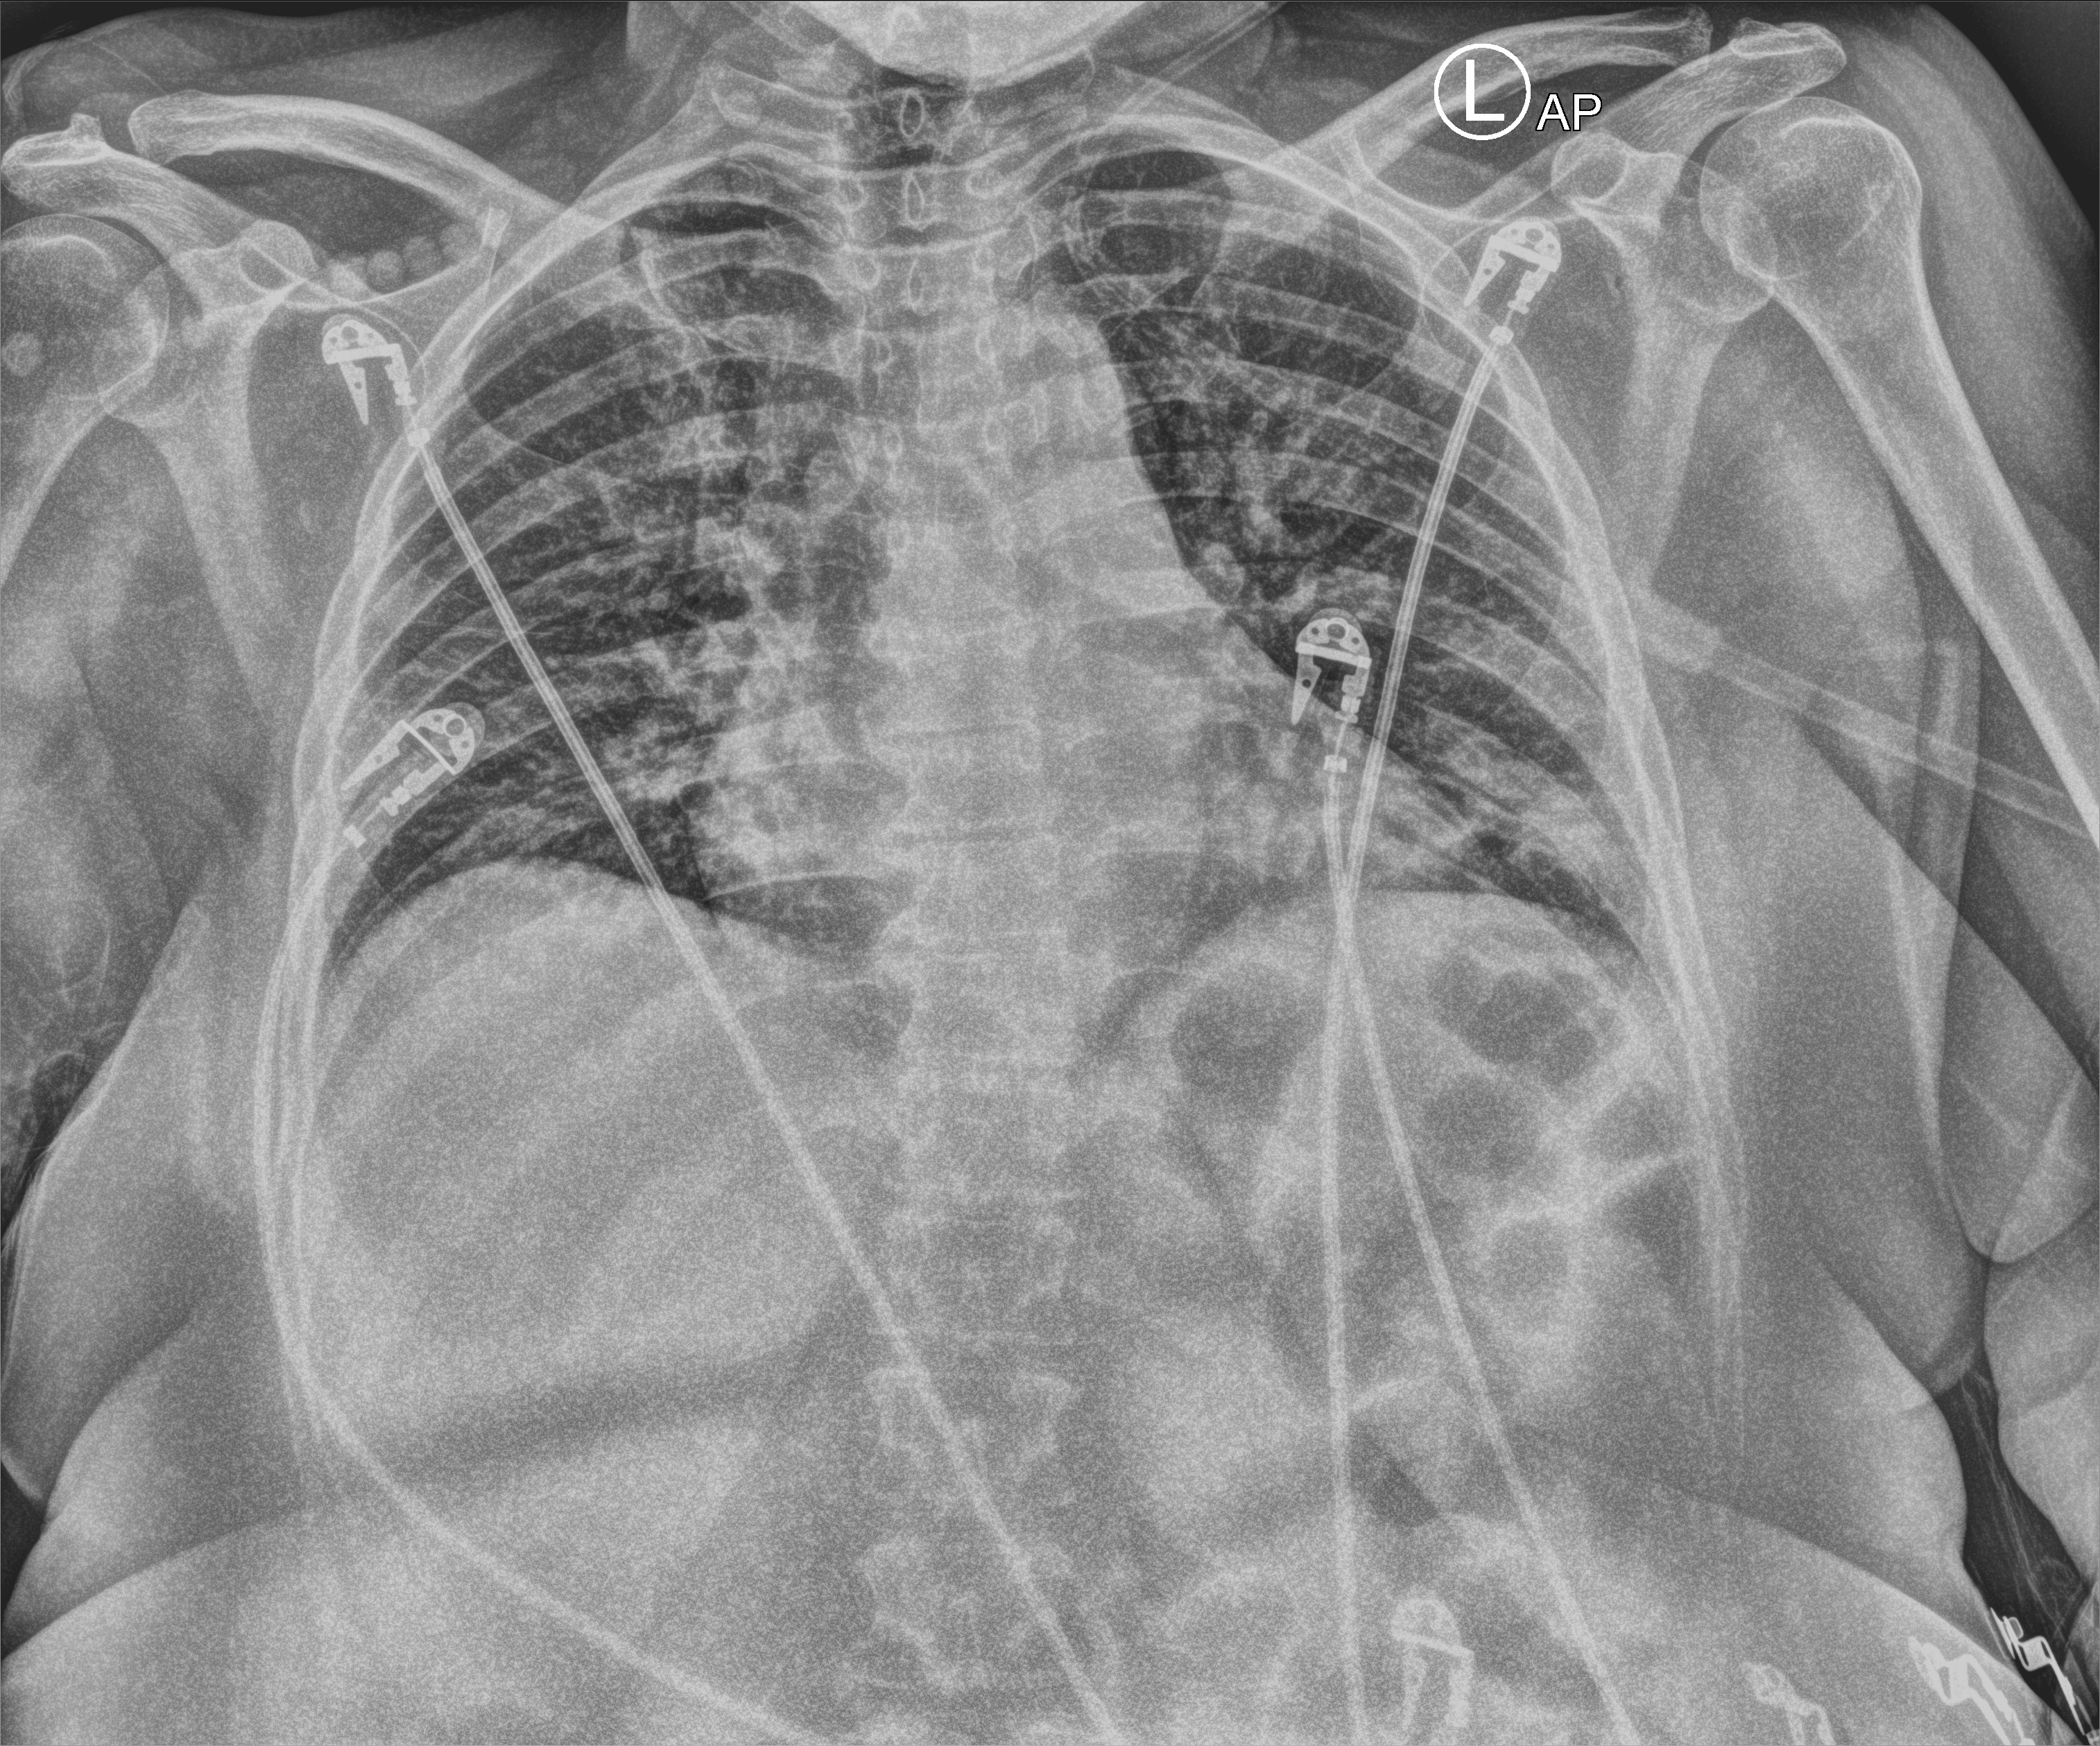
Bedside chest radiograph (computed radiography); anteroposterior (AP) projection. Patient hospitalised with COVID-19; female, aged 18–59 years.
Hospital-stay facts (about this admission, not read from this image; timing relative to this image not recorded): length of hospital stay: 6 days.